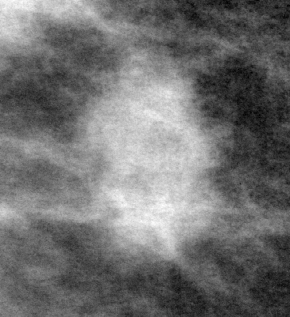
Cropped region of a digitized screen-film mammogram centred on a radiologist-marked abnormality, right breast, CC view.
- Mass, shape irregular, margins microlobulated; BI-RADS assessment category 4; subtlety rating 3 on a 1 (subtle) to 5 (obvious) scale; pathology result (as recorded, not read from the image): malignant.